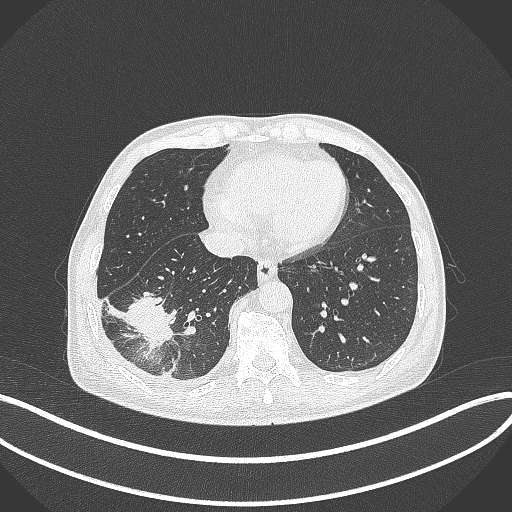
Chest CT, one axial slice. Position 113 of 388 along the scan axis. Reconstruction kernel B70f. 120 kVp. Lung window (W 1500 / L -600 HU). 512 × 512 image matrix, field of view 400 × 400 mm. Patient: male, 64 years. Case-level facts recorded for this patient, not image findings: clinical TNM (as recorded): T3 N0 M0; histopathological grade: G2-3.
Outlined on this slice (rectangle marked by the reading radiologist):
- lung tumour (recorded histology: adenocarcinoma): bounding box (x1, y1, x2, y2) in pixels: (123, 284, 180, 355)